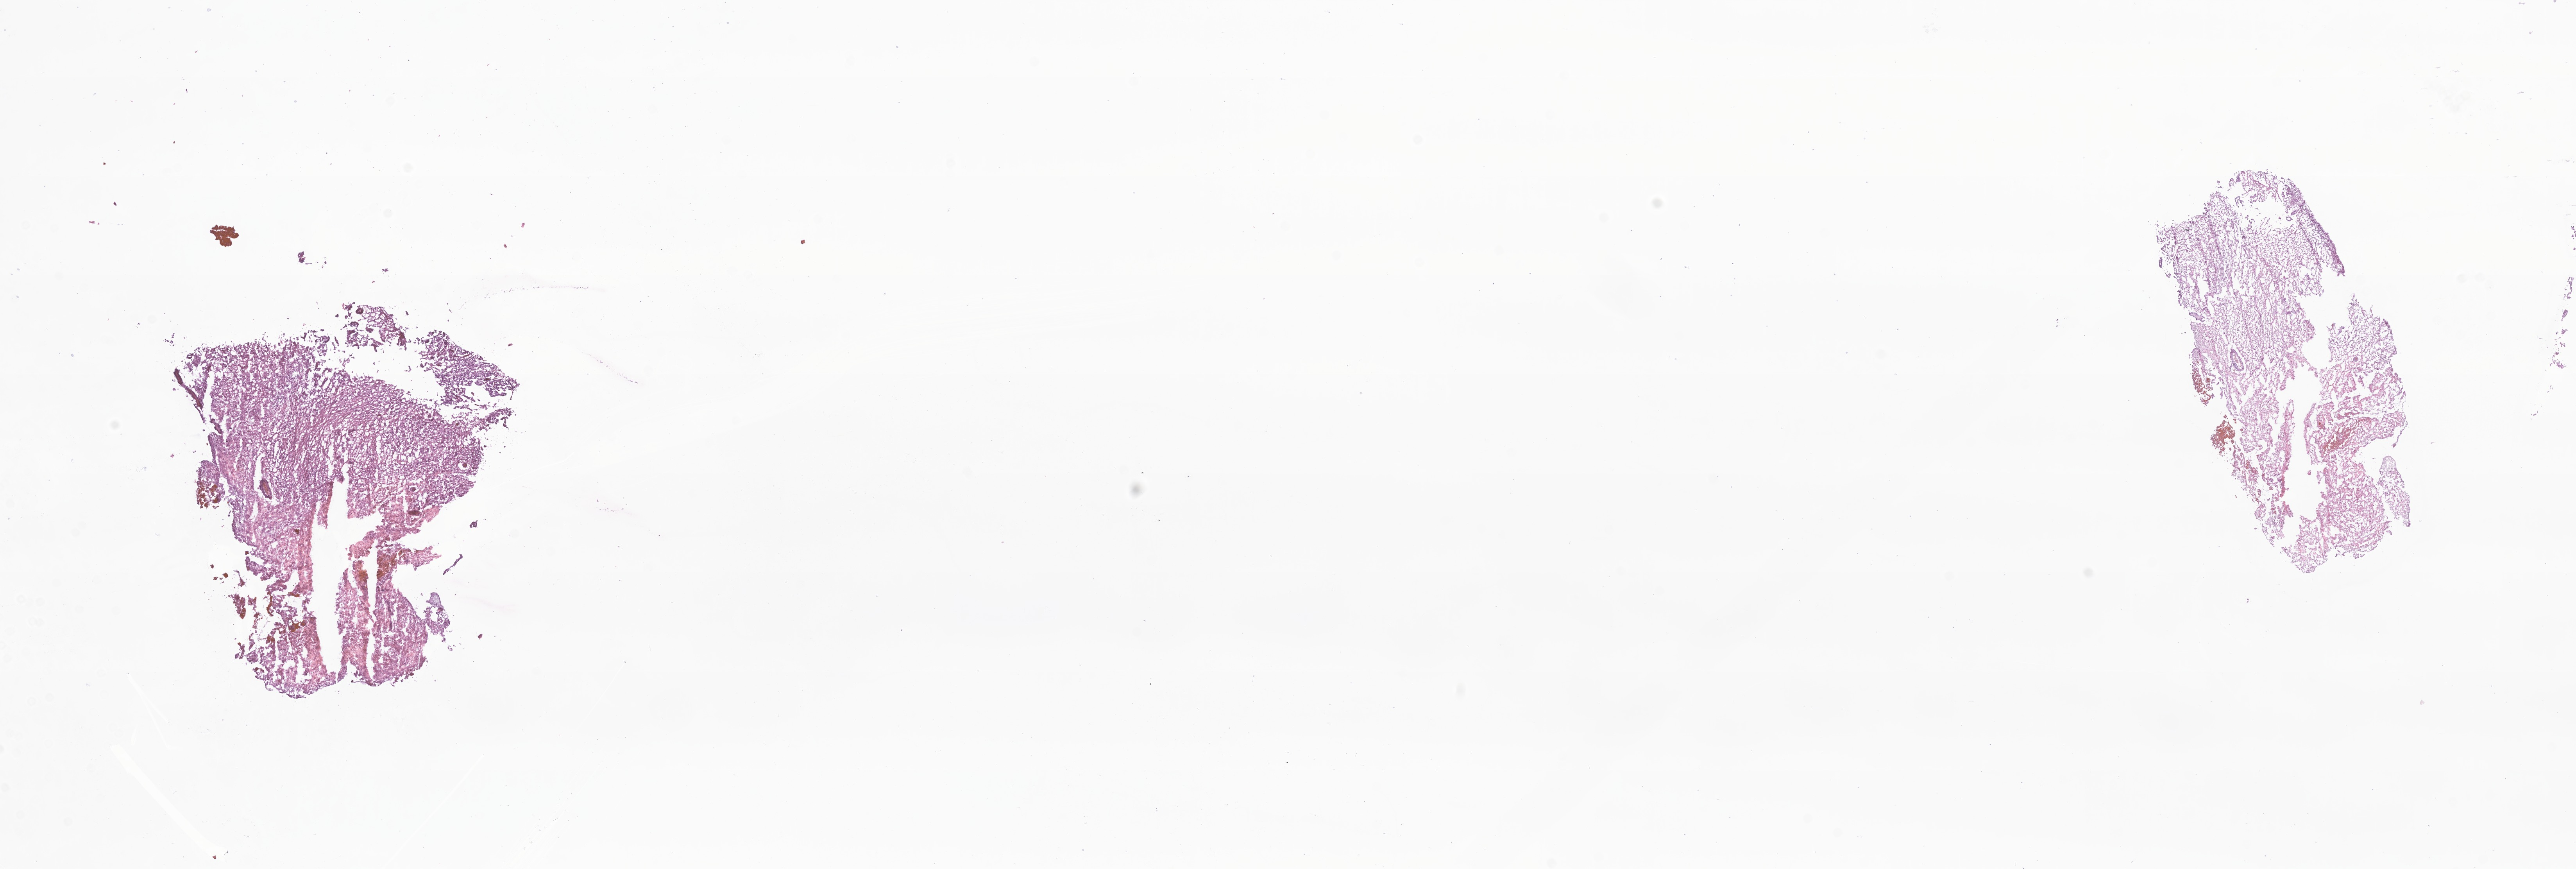
Digitized haematoxylin and eosin-stained section of tumor tissue from the temporal lobe, whole scanned area (about 27.8 x 9.4 mm) shown as a low-resolution overview. Frozen section. Male patient, age 190 months (15 years 10 months).
• diagnosis (ICD-O-3 morphology term): Tumor cells, uncertain whether benign or malignant